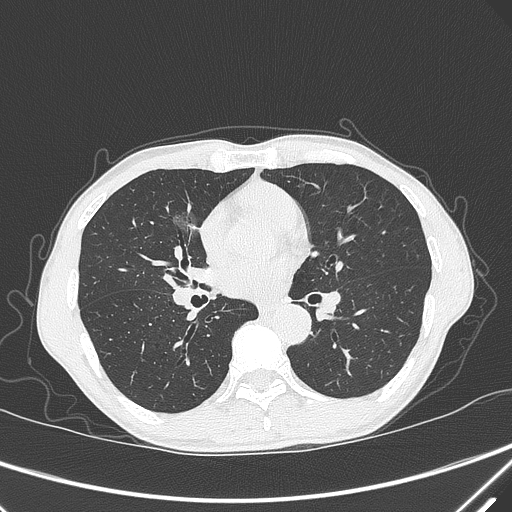
Chest CT, one axial slice; 120 kVp; lung window (W 1500 / L -600 HU); 1 mm slice thickness; 512 × 512 image matrix. Patient: male, 67 years. From the clinical record (not read from this slice): clinical TNM (as recorded): T1c N0 M0; histopathological grade: G1-2.
Annotated regions visible in this slice (bounding box drawn by a radiologist):
- lung tumour (recorded histology: adenocarcinoma): bounding box <157,199,196,244> (left, top, right, bottom; pixels)